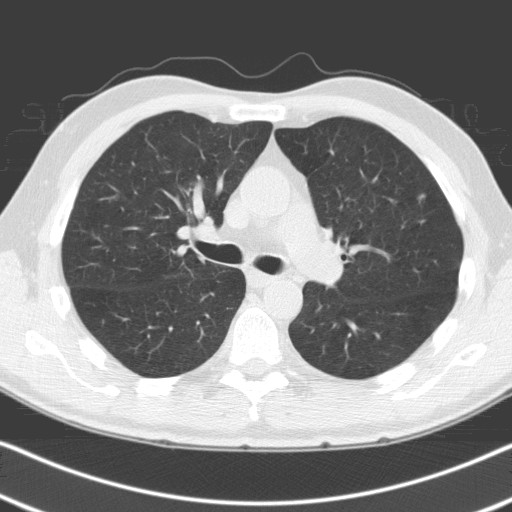
Low-dose screening chest CT, axial slice. Second annual screen. Lung window (W 1500 / L -600 HU). Standard (soft-tissue) reconstruction kernel (C). Slice 63 of 163 in the series. 512 × 512 image matrix, field of view 332 × 332 mm. Male, age 68 years at enrolment.
- Expert-annotated lung lesion, bounding box [x1, y1, x2, y2] px = [399, 180, 444, 225].
- Screening reader's record for this exam: no non-calcified nodule ≥4 mm recorded.
- Lung cancer was diagnosed 685 days after this screen: adenocarcinoma, NOS, left upper lobe, moderately differentiated (G2), stage IA (AJCC 6th edition), 6 mm at pathology.